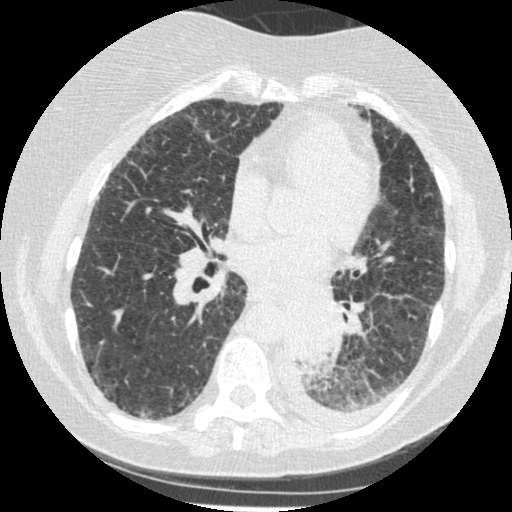
Low-dose screening chest CT, axial slice. Third screening round (two years after baseline). Lung window (W 1500 / L -600 HU). 1.25 mm slice thickness. Standard (soft-tissue) reconstruction kernel (STANDARD). 120 kVp. Slice 235 of 341 in the series. Female participant, aged 60 years at enrolment. Former smoker at enrolment.
Lesion marked by an expert reader, bounding box <275,304,342,376> (left, top, right, bottom; pixels). Reader record for this screening exam (exam-level; its link to the box is not recorded): non-calcified nodule or mass ≥4 mm, left lower lobe, 54 × 38 mm, smooth margins, soft tissue attenuation, pre-existing on the prior screen: yes; interval growth: yes.